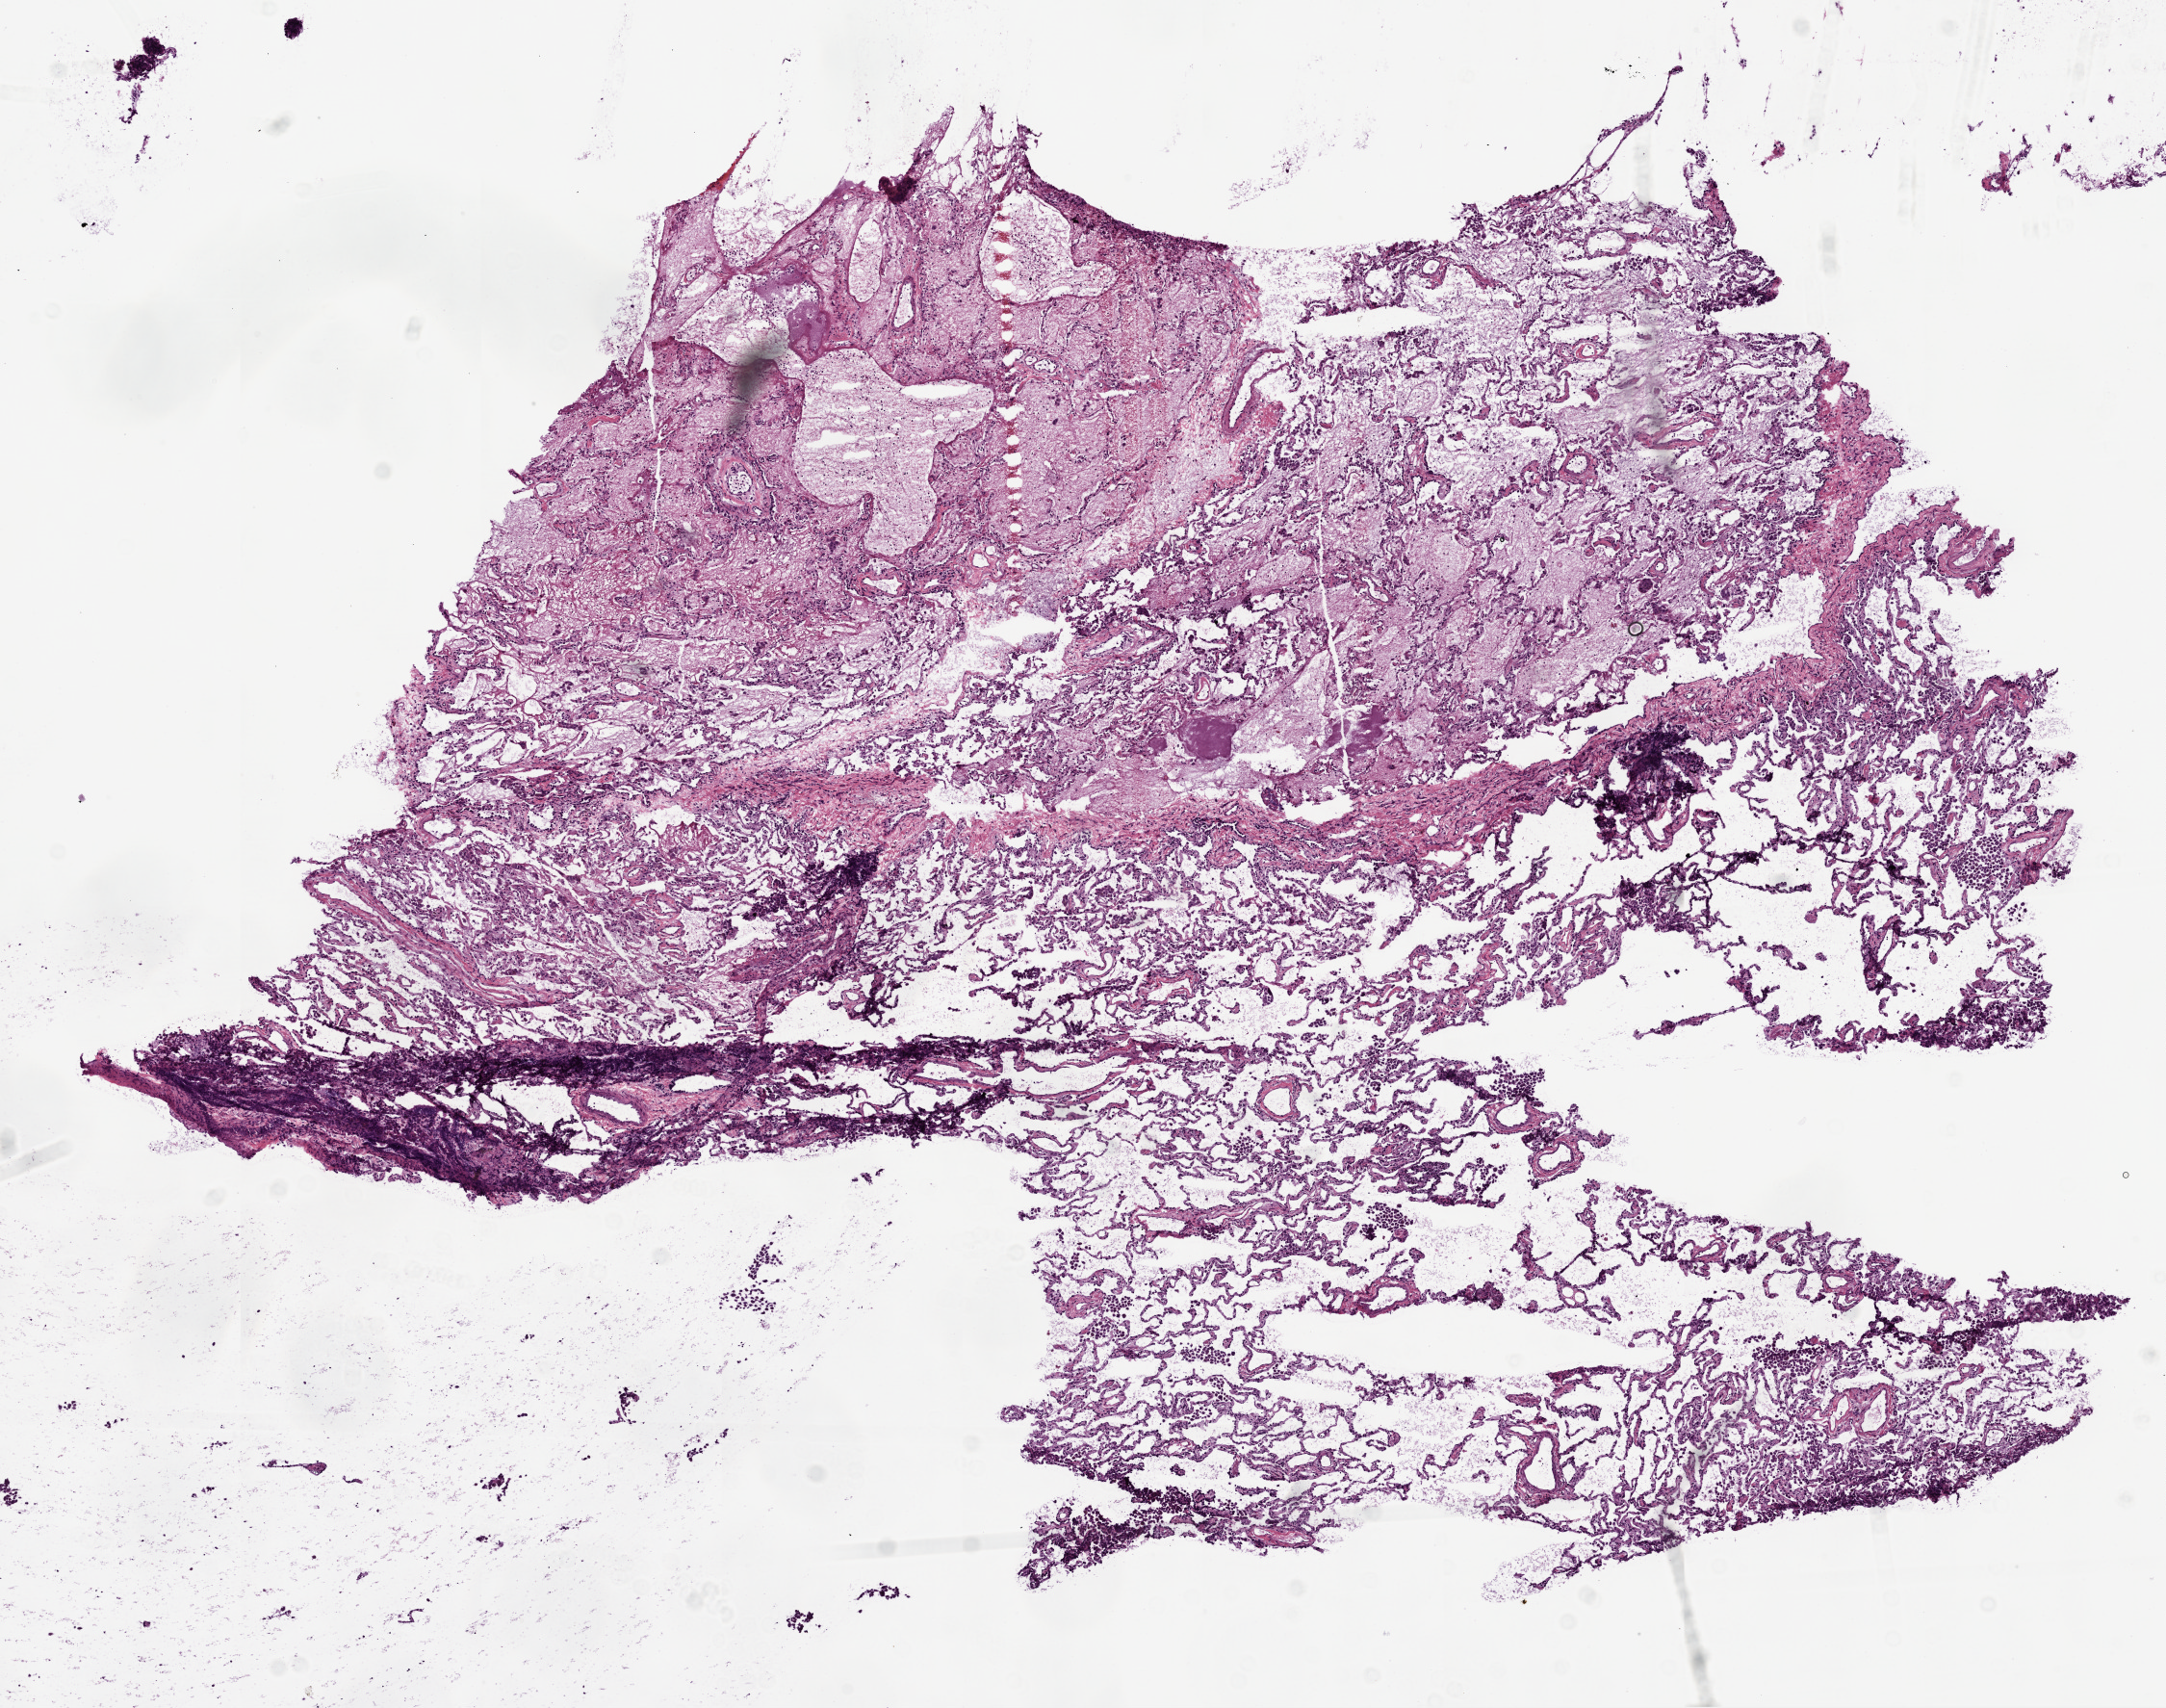
Digitized H&E tissue section (whole slide) — low-resolution overview of the scanned area, about 9.0 x 7.1 mm (acquisition: 20x scan); frozen section from the top of the tissue portion; sample: solid tissue normal (non-tumour tissue), lung. Female patient; age at initial diagnosis 66 years.
* this section: solid tissue normal (non-tumour) sample from the same patient
* patient diagnosis: Squamous cell carcinoma, NOS